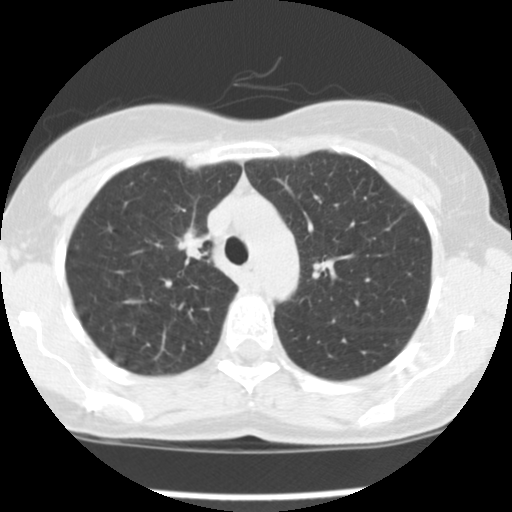
Low-dose screening chest CT, one axial slice. Slice 114 of 157 in the series (ordered by position). Lung window (W 1500 / L -600 HU). 512 × 512 image matrix, field of view 282 × 282 mm.
Annotated regions visible in this slice (manually delineated by an expert):
- lesion 1 (tumor, upper lobe of right lung): bounding box <179,228,205,260> (left, top, right, bottom; pixels)